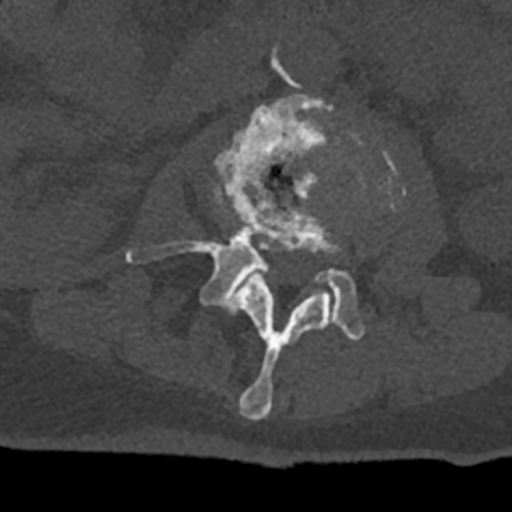
CT including the spine, one axial slice; slice 348 of 797 in the series (ordered by position); bone window (W 1800 / L 400 HU); 0.5 mm slice thickness; 512 × 512 image matrix. Patient: male, 74 years. Case-level facts recorded for this patient, not image findings: primary cancer: renal.
Structures marked on this image (semi-automatically segmented with operator editing):
- L2 vertebra: bounding box [x1, y1, x2, y2] px = [229, 191, 330, 420]
- L3 vertebra: [125, 94, 393, 341]